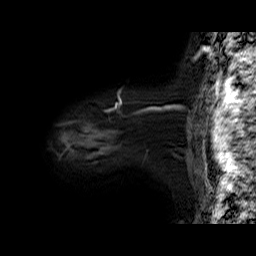
Breast MRI (dynamic contrast-enhanced), one sagittal slice; position 57 of 60 along the scan axis; dynamic contrast-enhanced series, time point 2 of 6 at this slice position (early post-contrast); 1.5 T; TE 6.3 ms, TR 32.9 ms; 4 mm slice thickness; 256 × 256 image matrix. Female patient. From the clinical record (not read from this slice): setting: breast cancer imaged before/during neoadjuvant chemotherapy; receptor status: HER2-positive.
Structures marked on this image (semi-automatically segmented with operator editing):
- analysis volume of interest (the breast-tissue region the enhancement analysis was run in; not a lesion): bounding box <60,98,179,165> (left, top, right, bottom; pixels)
- tumour enhancement mask (voxels above the 100 % enhancement threshold inside the analysis volume of interest): <118,102,159,114>